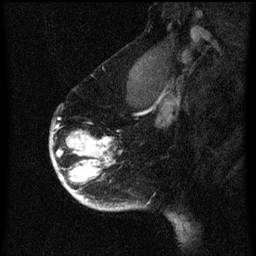
Breast MRI (dynamic contrast-enhanced), one sagittal slice. Slice 48 of 60 in the series (ordered by position). Dynamic contrast-enhanced series, image 2 of 3 at this slice position (ordered by acquisition). 1.5 T. TE 4.2 ms, TR 8 ms. 2 mm slice thickness. 256 × 256 image matrix. Female patient, age 56 years.
Annotated regions visible in this slice (semi-automatic segmentation, software-assisted and operator-edited):
- analysis volume of interest (the breast-tissue region the enhancement analysis was run in; not a lesion): box from (x=52, y=132) to (x=125, y=213) px
- tumour enhancement mask (voxels above the 70 % enhancement threshold inside the analysis volume of interest): (x=52, y=132)–(x=123, y=211)